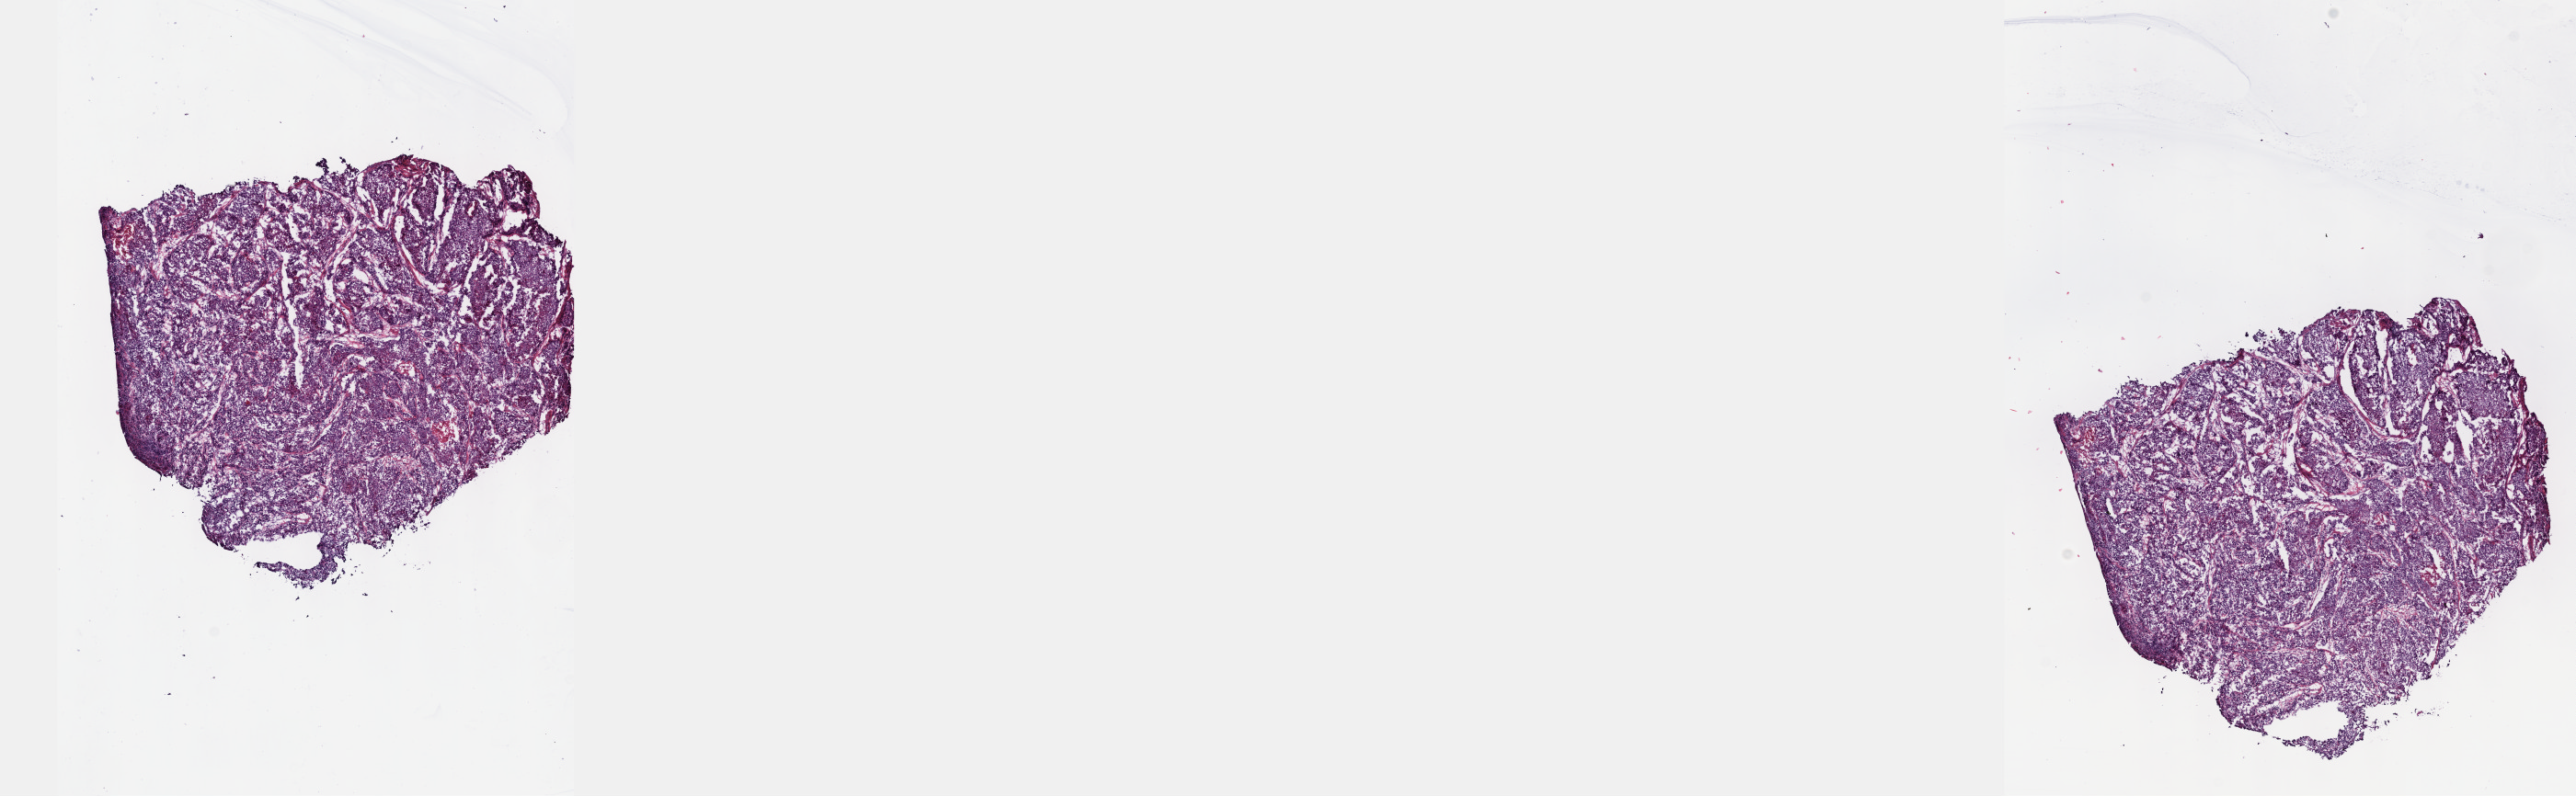
Digitized H&E-stained tissue section (whole slide) — whole scanned area (about 22.6 x 7.0 mm, slide scanned at 40x) shown as a low-resolution overview; frozen section from the top of the tissue portion; primary tumour sample from the cervix. Patient: female, age at initial diagnosis 79 years. Histologic grade: G2 (moderately differentiated). Composition of this section per pathologist review: tumour cells 90%, tumour nuclei 90%, normal cells 2%, stromal cells 8%, necrosis 0%. Inflammatory infiltration, as recorded: lymphocyte infiltration 2%, monocyte infiltration 0%, neutrophil infiltration 0%.
- lymph nodes positive (case pathology): 3 of 23 examined
- FIGO stage: IB1
- pathologic diagnosis: Squamous cell carcinoma, NOS (cervix uteri)